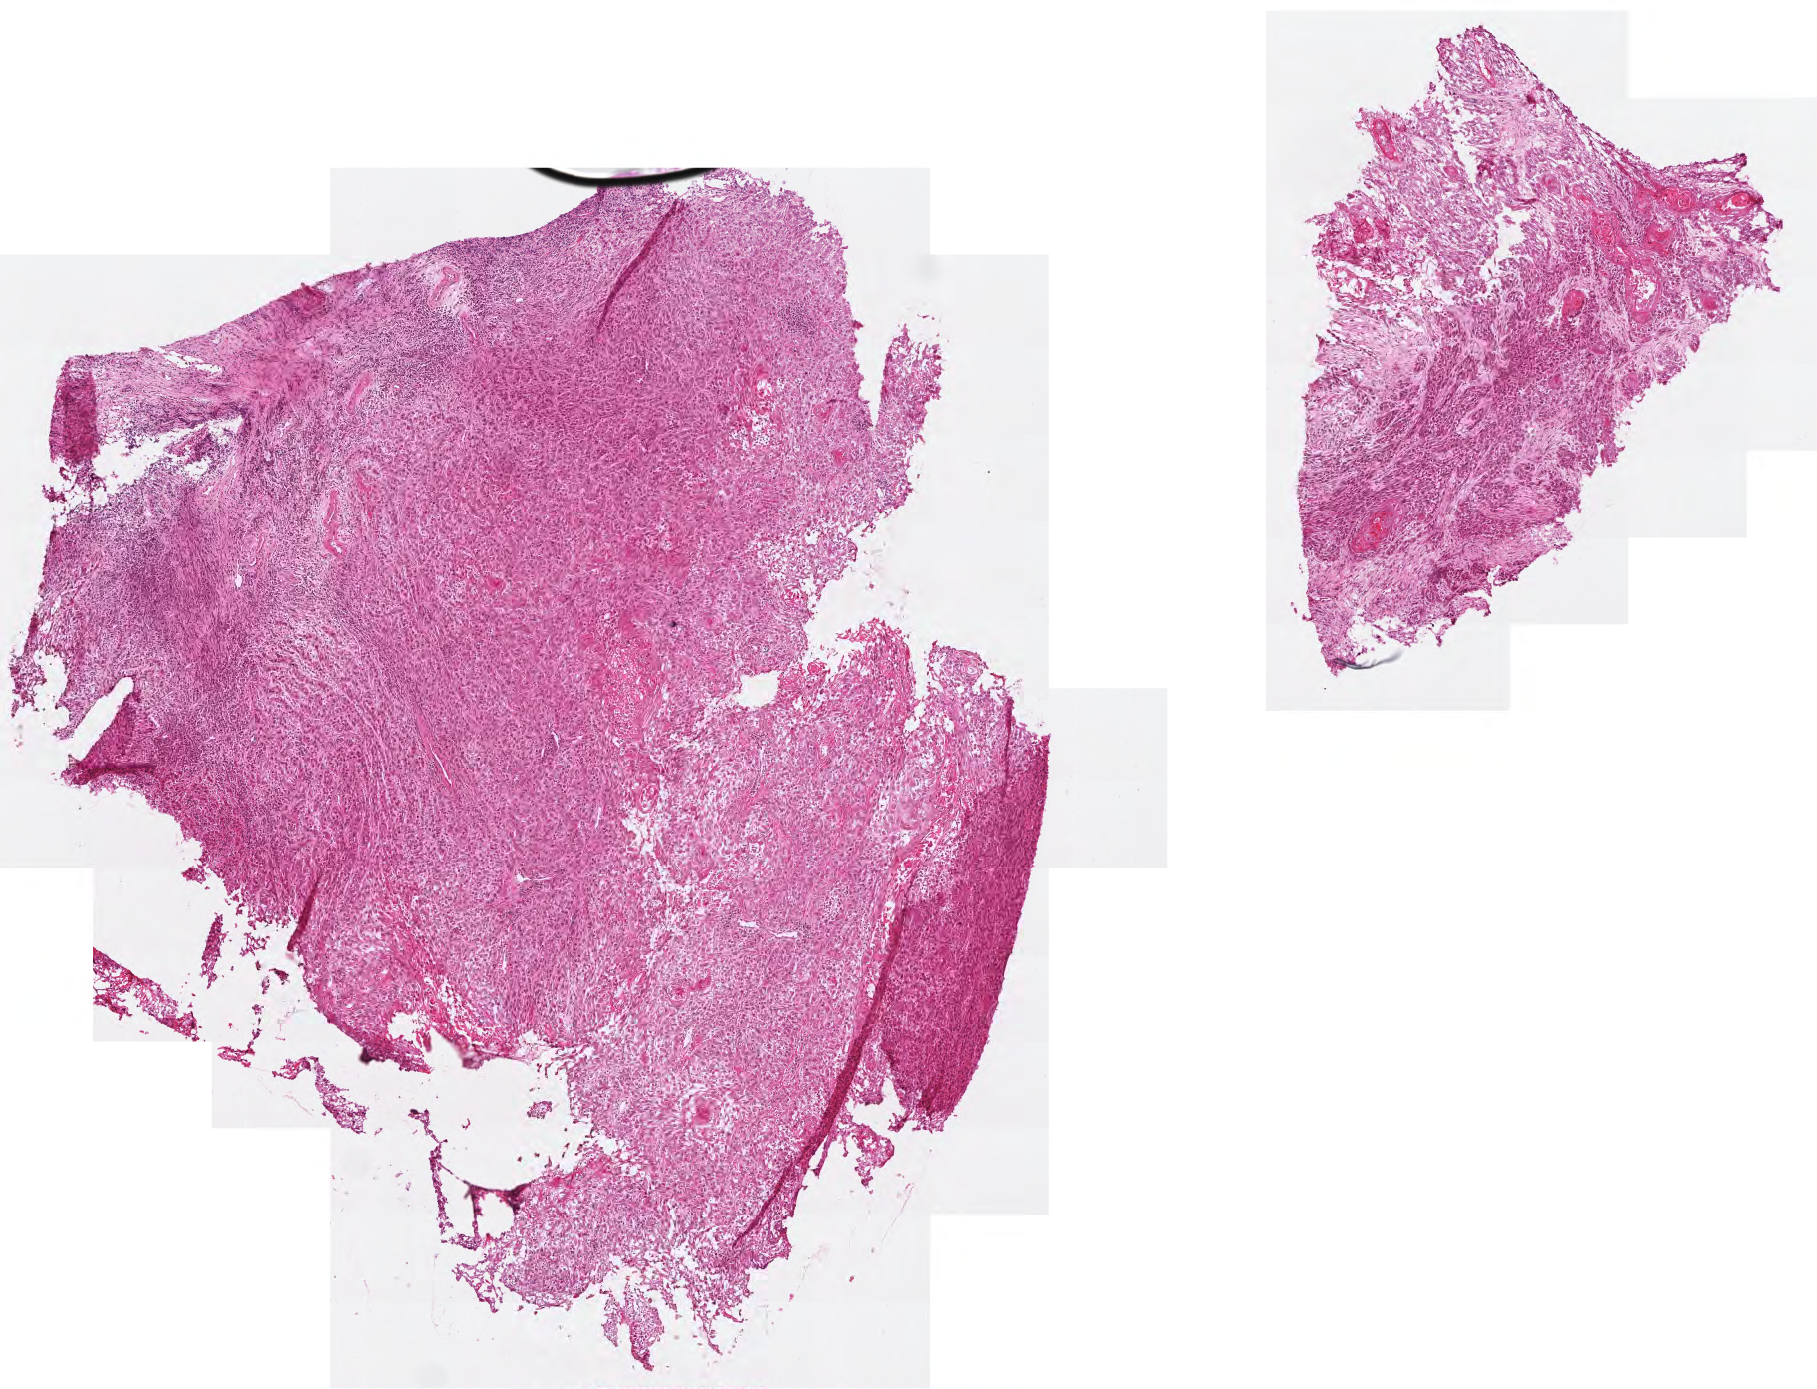
H&E-stained whole-slide image — low-resolution overview of the scanned area, about 3.6 x 2.8 mm; frozen section from the top of the tissue portion; sample: primary tumour, head and neck. Female patient; age at initial diagnosis 66 years. Histologic grade: G3 (poorly differentiated). Composition of this section per pathologist review: tumour cells 85%, tumour nuclei 80%, normal cells 0%, stromal cells 15%, necrosis 0%.
Diagnosis: Squamous cell carcinoma, NOS (tonsil, NOS).